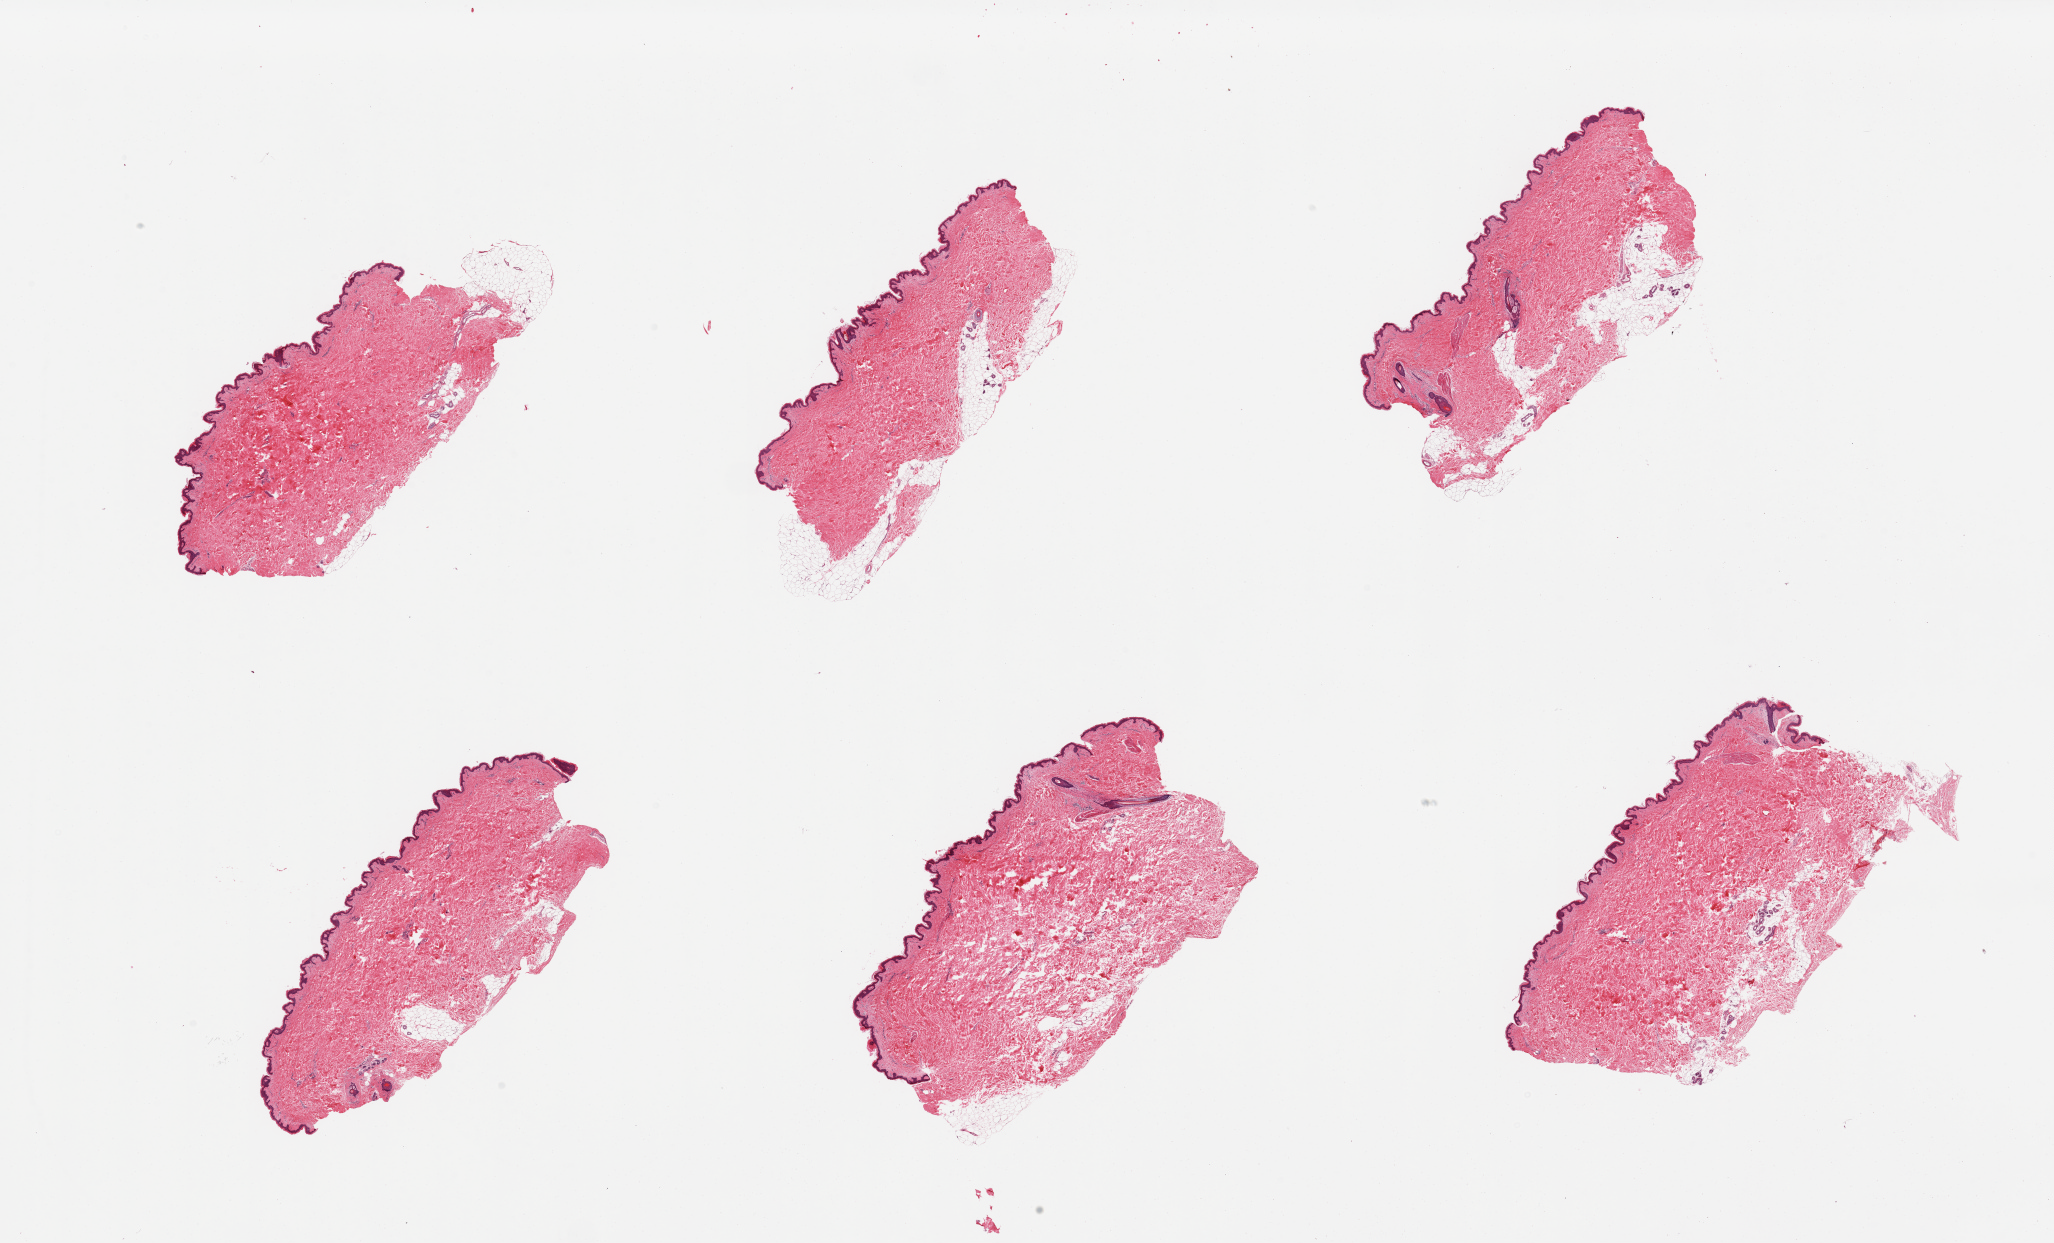
Digitized H&E-stained section — shown as a low-resolution overview of the whole scanned area (about 32.5 x 19.7 mm); PAXgene-fixed, paraffin-embedded tissue; target tissue: skin of suprapubic region; donor tissue sample. Donor: female.
Reviewer comment on this tissue sample: 6 pieces, minimal adherent dermal fat; Squamous epithelium is ~40-50 microns thick.